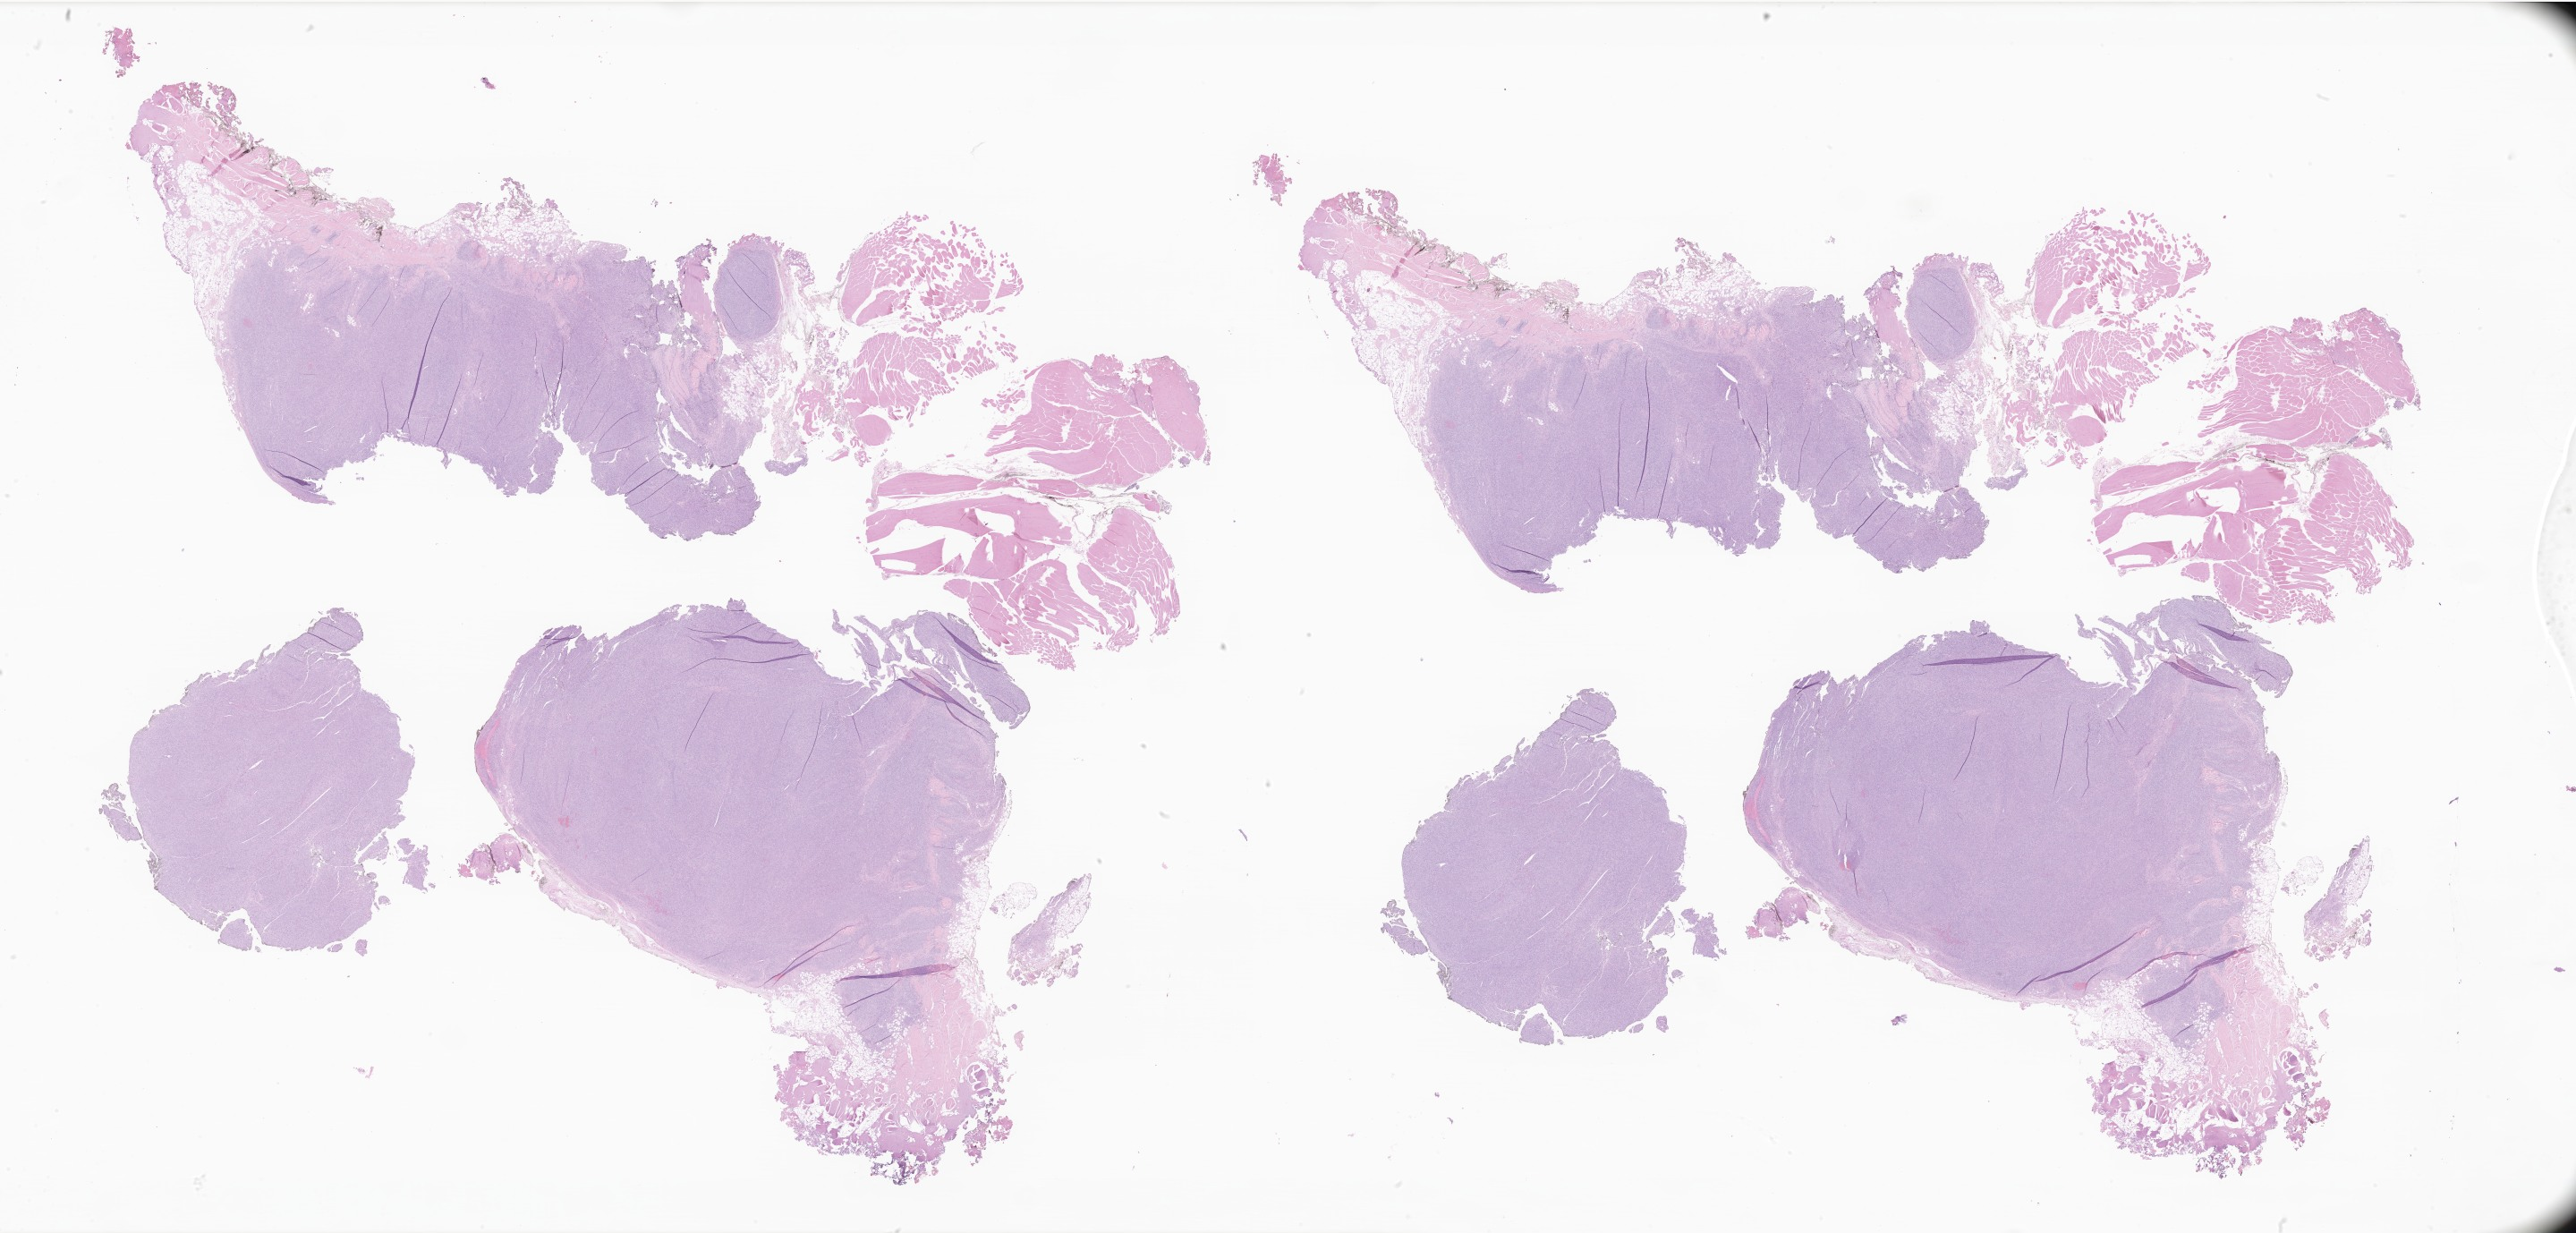
Whole-slide image, H&E stain of tumor tissue from the soft tissue of abdomen, shown as a low-resolution overview of the whole scanned area (about 48.5 x 23.2 mm); formalin-fixed paraffin-embedded section. Patient male; age 191 months (15 years 11 months).
Recorded diagnosis: Rhabdomyosarcoma, NOS.